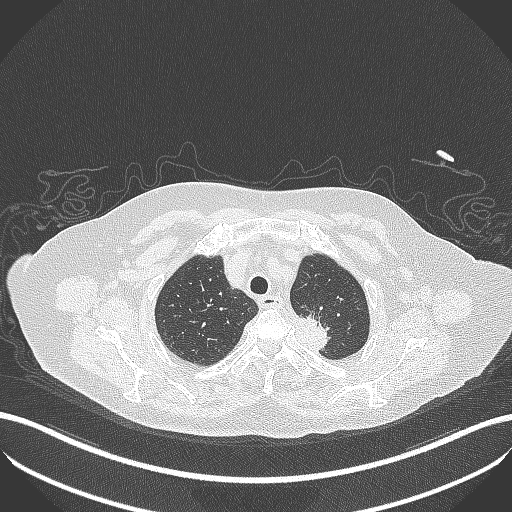
Chest CT, one axial slice; slice 288 of 353 in the series (ordered by position); 100 kVp; lung window (W 1500 / L -600 HU); 1 mm slice thickness; 512 × 512 image matrix, field of view 400 × 400 mm. Female patient, age 81 years. From the clinical record (not read from this slice): clinical TNM (as recorded): T2a N0 M0.
Structures marked on this image (rectangle marked by the reading radiologist):
- lung tumour (recorded histology: adenocarcinoma): bounding box (x1, y1, x2, y2) in pixels: (287, 307, 337, 354)